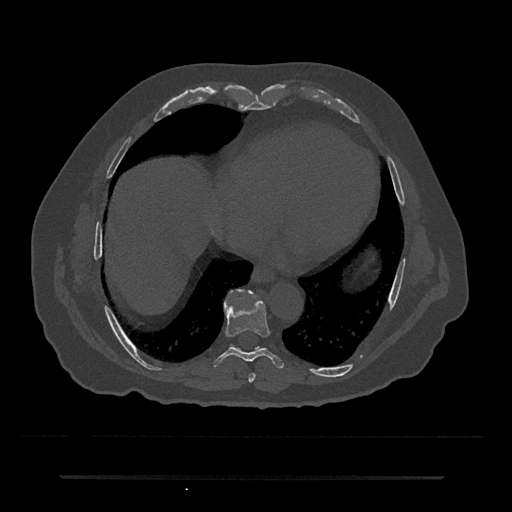
CT including the spine, one axial slice. Slice 325 of 797 in the series (ordered by position). Reconstruction kernel Br40s/3. Bone window (W 1800 / L 400 HU). 0.5 mm slice thickness. 512 × 512 image matrix. Patient: male, 69 years. From the clinical record (not read from this slice): primary cancer: prostate.
Annotated regions visible in this slice (semi-automatic segmentation, software-assisted and operator-edited):
- T7 vertebra: bounding box (x1, y1, x2, y2) in pixels: (248, 373, 256, 383)
- T8 vertebra: (213, 299, 284, 368)
- T9 vertebra: (238, 290, 244, 293)